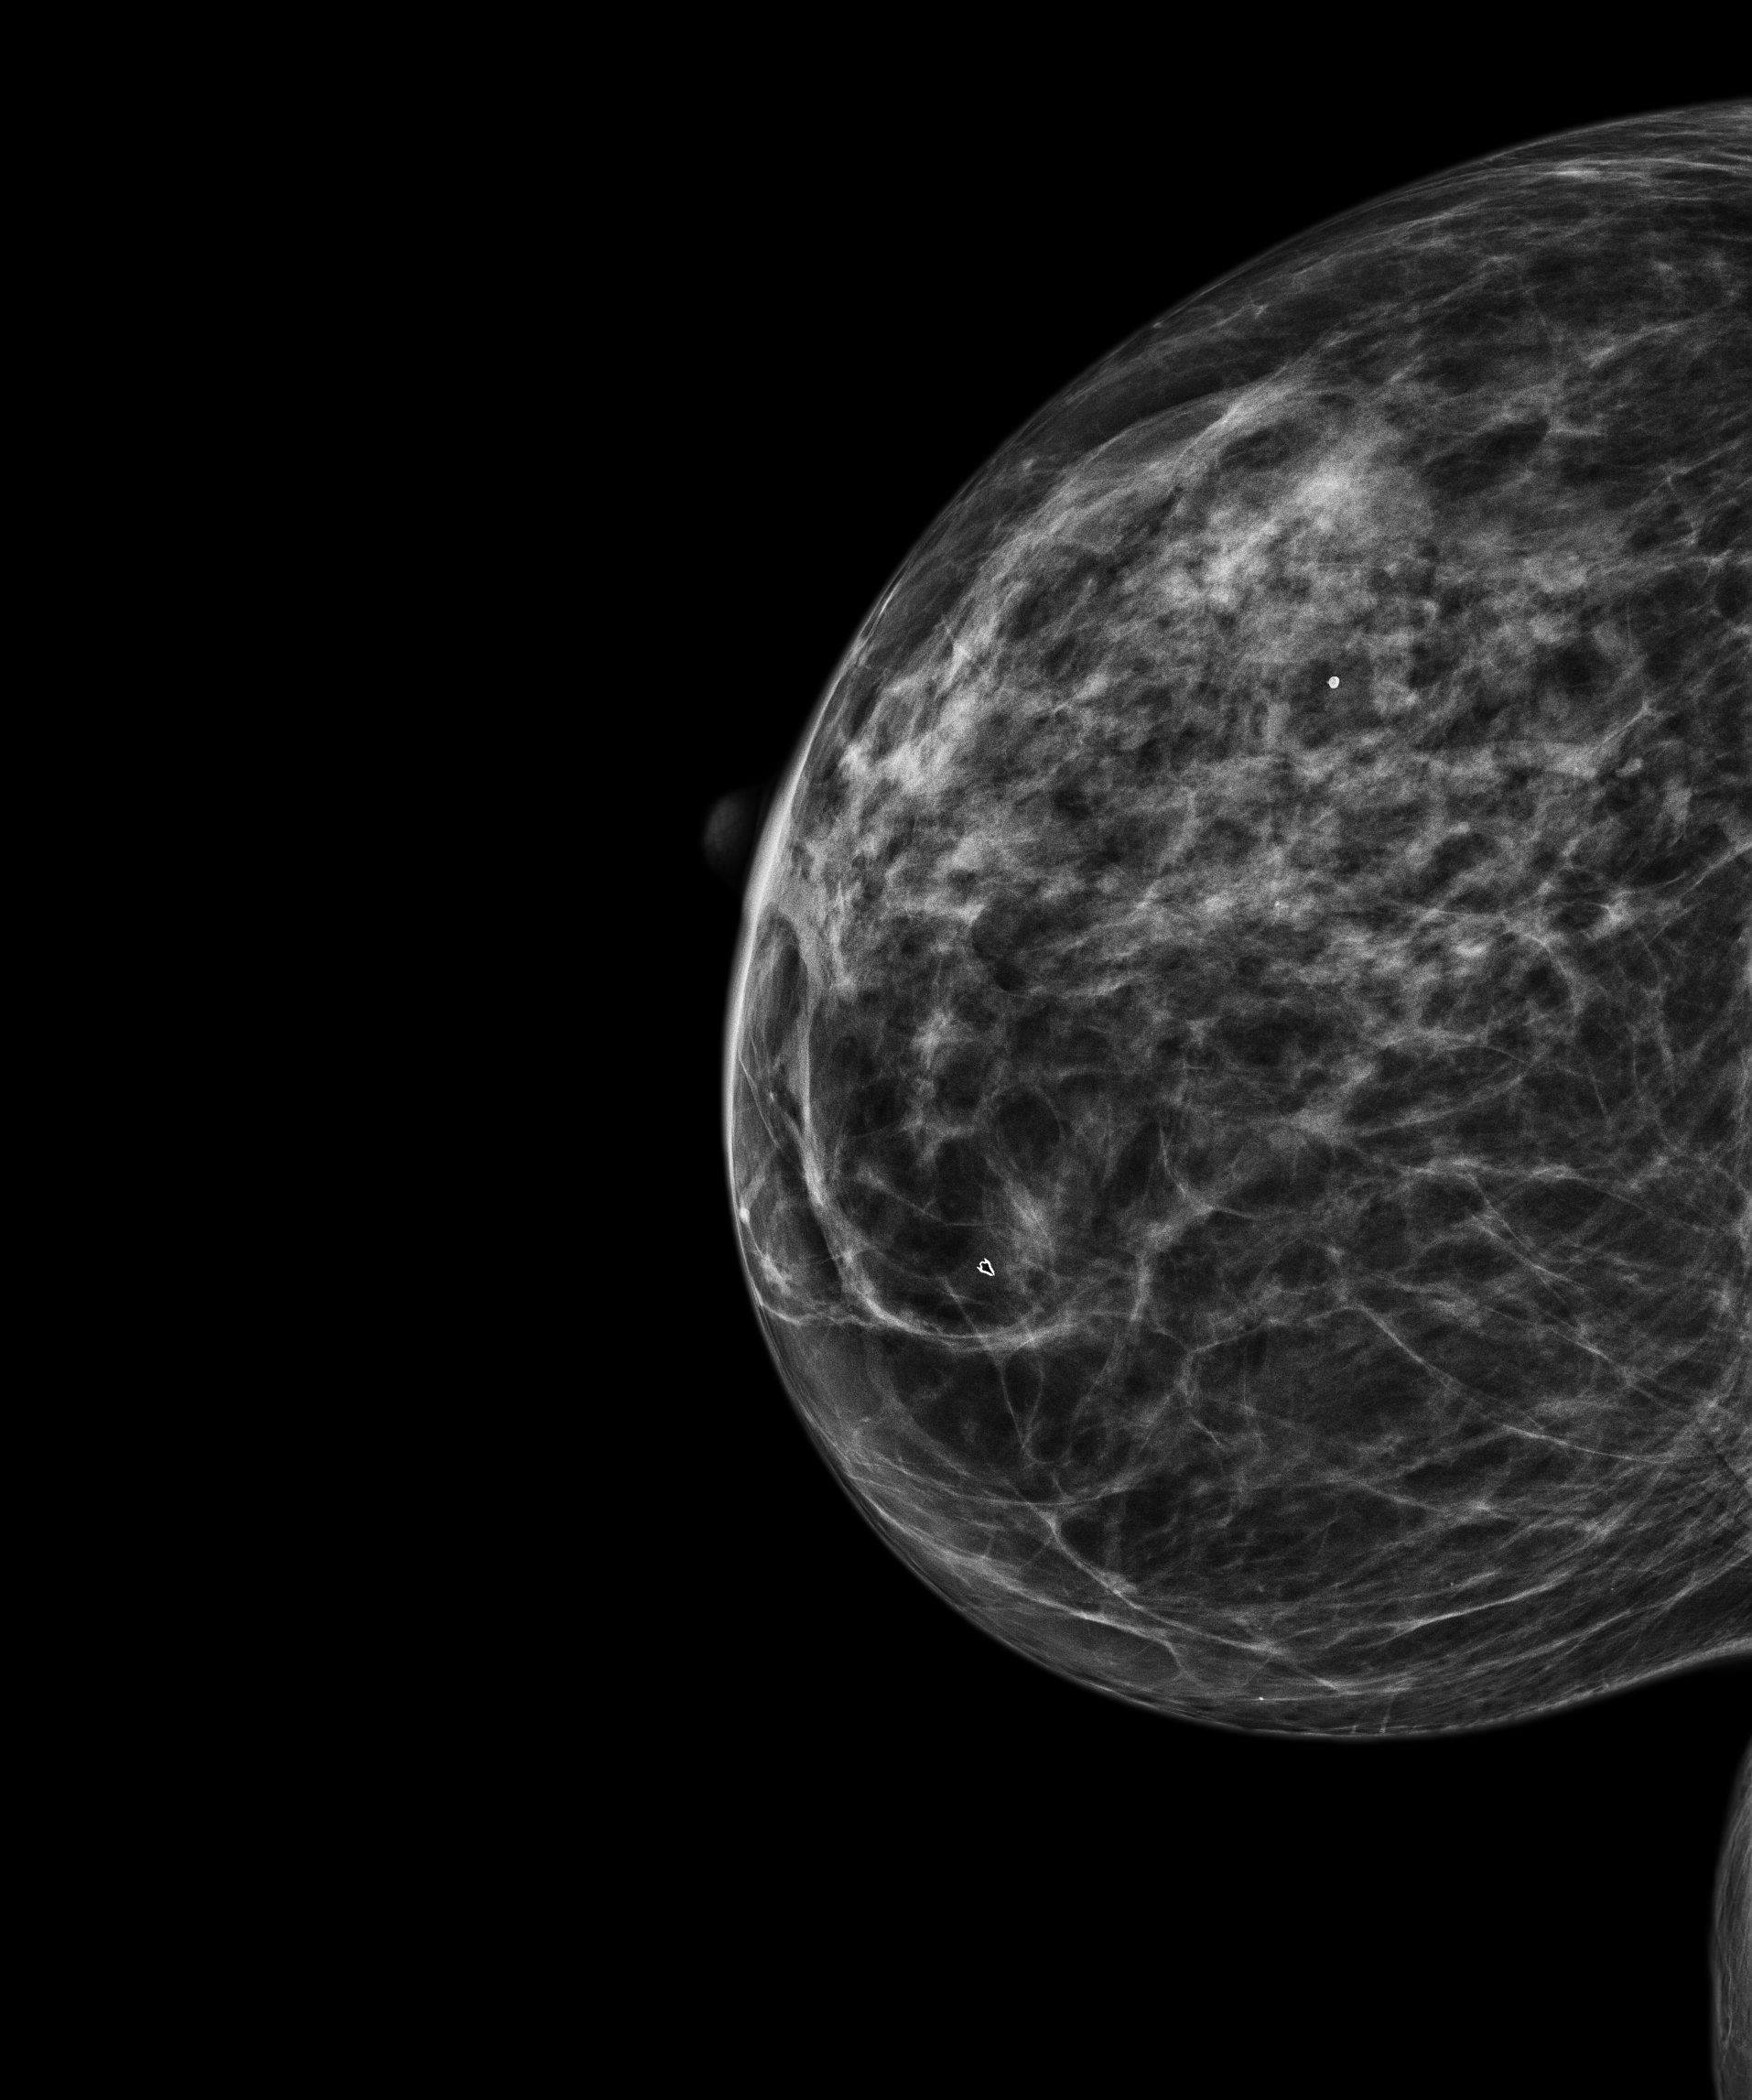
Screening examination; compressed breast thickness 41.5 mm.
Image type: full-field digital mammogram. Breast: right. Projection: CC view.